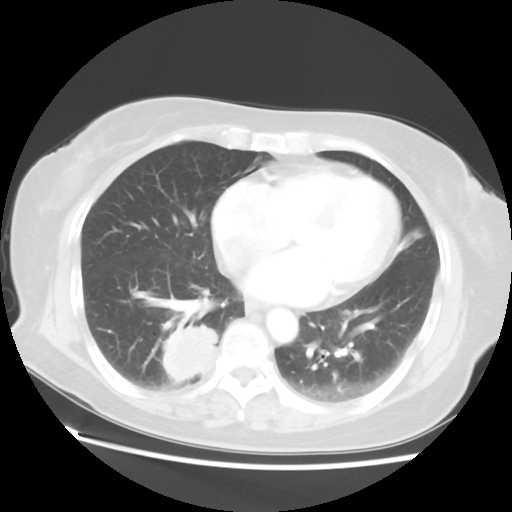
Chest CT, one axial slice. Slice 21 of 52 in the series (ordered by position). Reconstruction kernel STANDARD. Lung window (W 1500 / L -600 HU). 5 mm slice thickness. 512 × 512 image matrix, field of view 356 × 356 mm. Patient: female, 69 years. Case-level facts recorded for this patient, not image findings: clinical TNM (as recorded): T2 N1 M1a.
Structures marked on this image (bounding box drawn by a radiologist):
- lung tumour (recorded histology: adenocarcinoma): bounding box (x1, y1, x2, y2) in pixels: (160, 323, 222, 389)